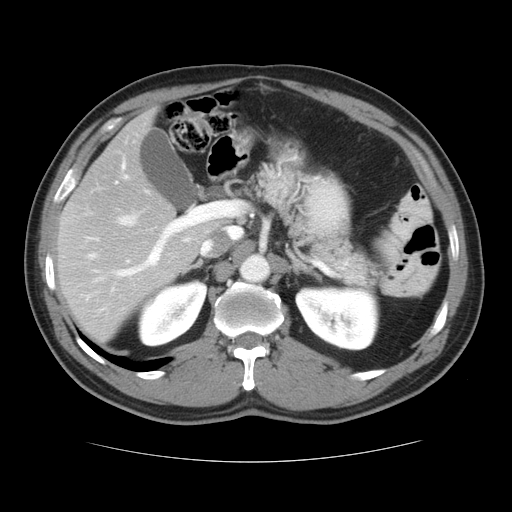
Contrast-enhanced abdominal CT, one axial slice. Slice 21 of 37 in the series (ordered by position). Reconstruction kernel STANDARD. Soft-tissue window (W 400 / L 40 HU). 512 × 512 image matrix. Male patient, age 66 years. Case-level facts recorded for this patient, not image findings: diagnosis: colorectal cancer liver metastases, imaged before liver resection; multiple liver metastases: yes; largest metastasis: 1.6 cm; disease in both lobes: yes.
Structures marked on this image (expert manual segmentation):
- hepatic veins: bounding box (x1, y1, x2, y2) in pixels: (93, 174, 238, 263)
- liver: (58, 112, 219, 343)
- planned liver remnant (the part of the liver to remain after resection): (58, 202, 220, 343)
- portal vein (with intrahepatic branches): (94, 157, 214, 281)